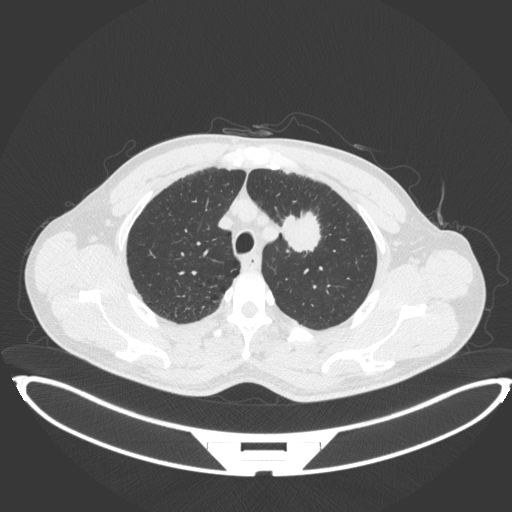
Chest CT, one axial slice; slice 348 of 407 in the series (ordered by position); reconstruction kernel B31f; lung window (W 1500 / L -600 HU); 1 mm slice thickness; 512 × 512 image matrix. Male patient, age 60 years. From the clinical record (not read from this slice): clinical TNM (as recorded): T2a N0 M0; histopathological grade: G1-G2.
Outlined on this slice (bounding box drawn by a radiologist):
- lung tumour (recorded histology: squamous cell carcinoma): bounding box <281,209,324,254> (left, top, right, bottom; pixels)